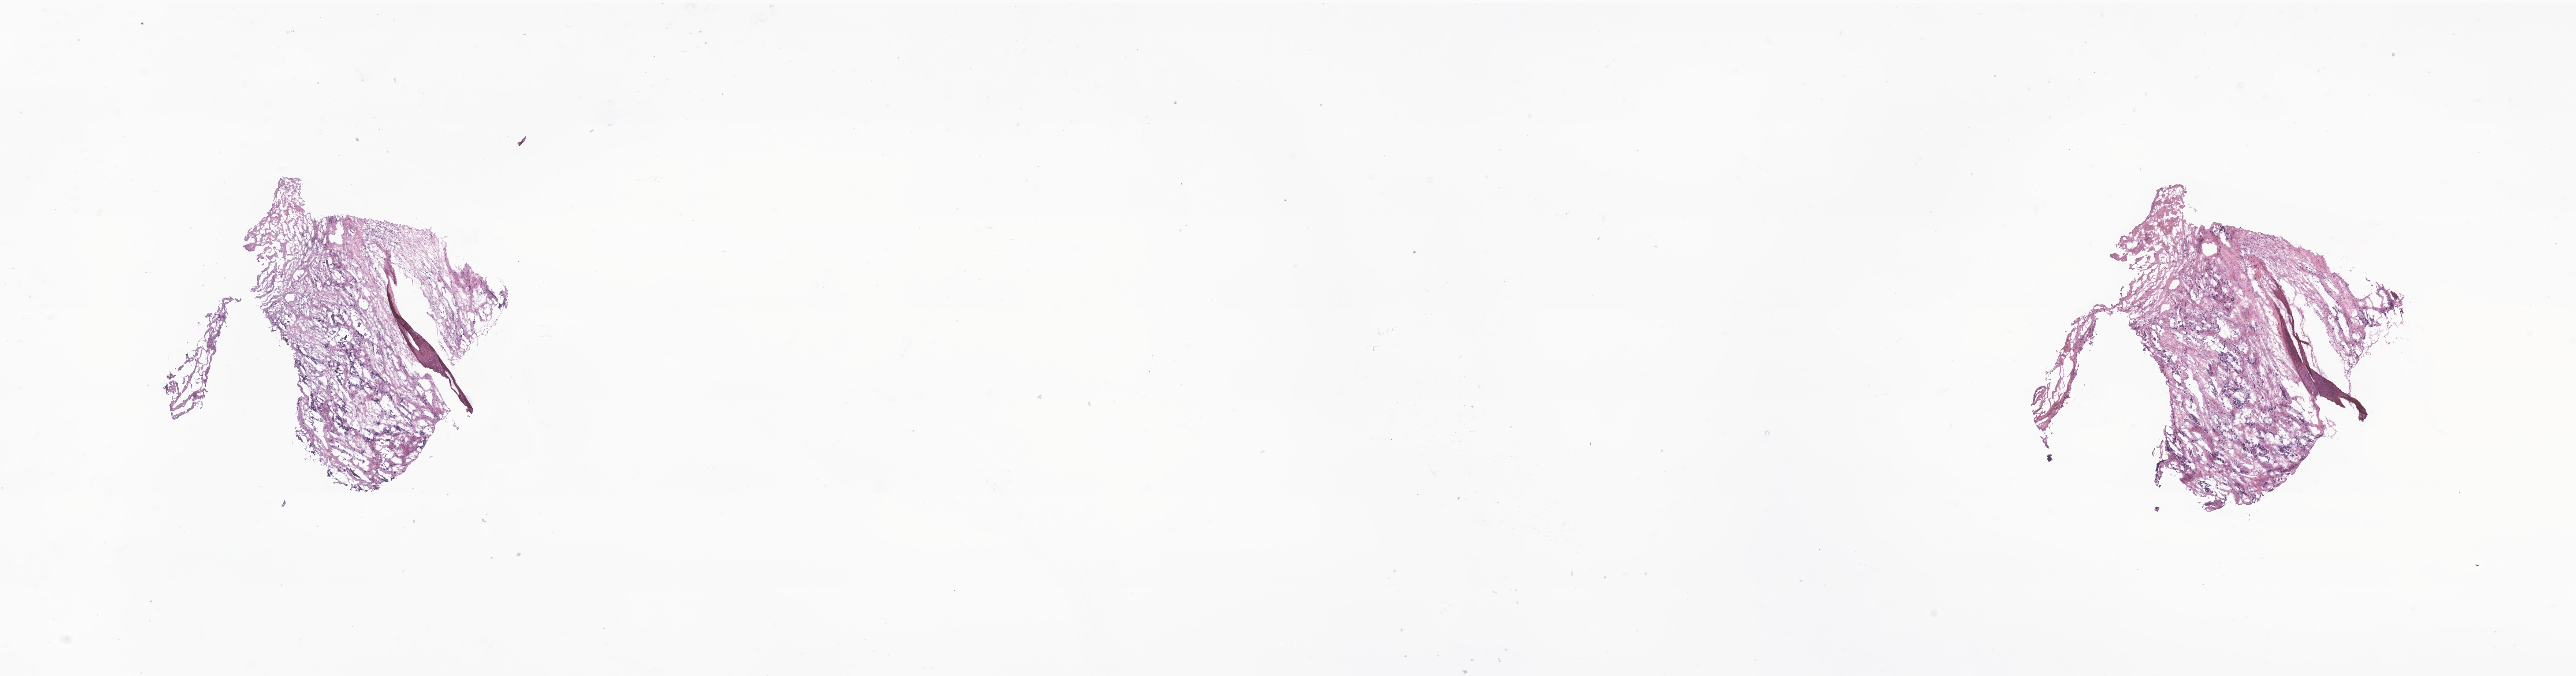
Digitized haematoxylin and eosin-stained section of tumor tissue from the adrenal gland — low-resolution overview of the scanned area, about 29.7 x 7.8 mm; frozen section. Male patient, age 454 days (about 1.2 years).
Recorded diagnosis: Neuroblastoma, NOS.